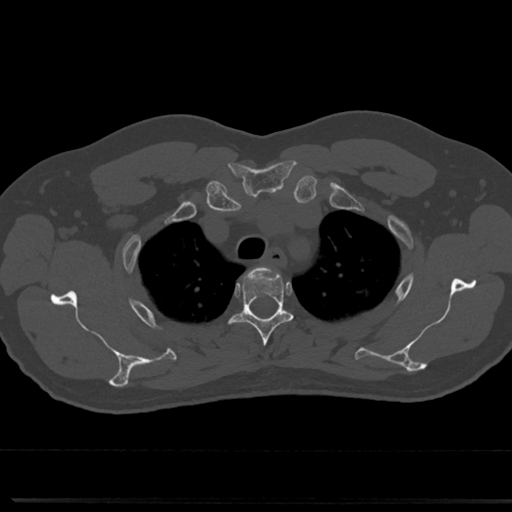
CT including the spine, one axial slice; position 592 of 817 along the scan axis; reconstruction kernel Br40s/3; bone window (W 1800 / L 400 HU); 0.5 mm slice thickness; 512 × 512 image matrix. Male patient, age 61 years. From the clinical record (not read from this slice): primary cancer: prostate.
Outlined on this slice (semi-automatically segmented with operator editing):
- T3 vertebra: bounding box [x1, y1, x2, y2] px = [235, 266, 292, 365]